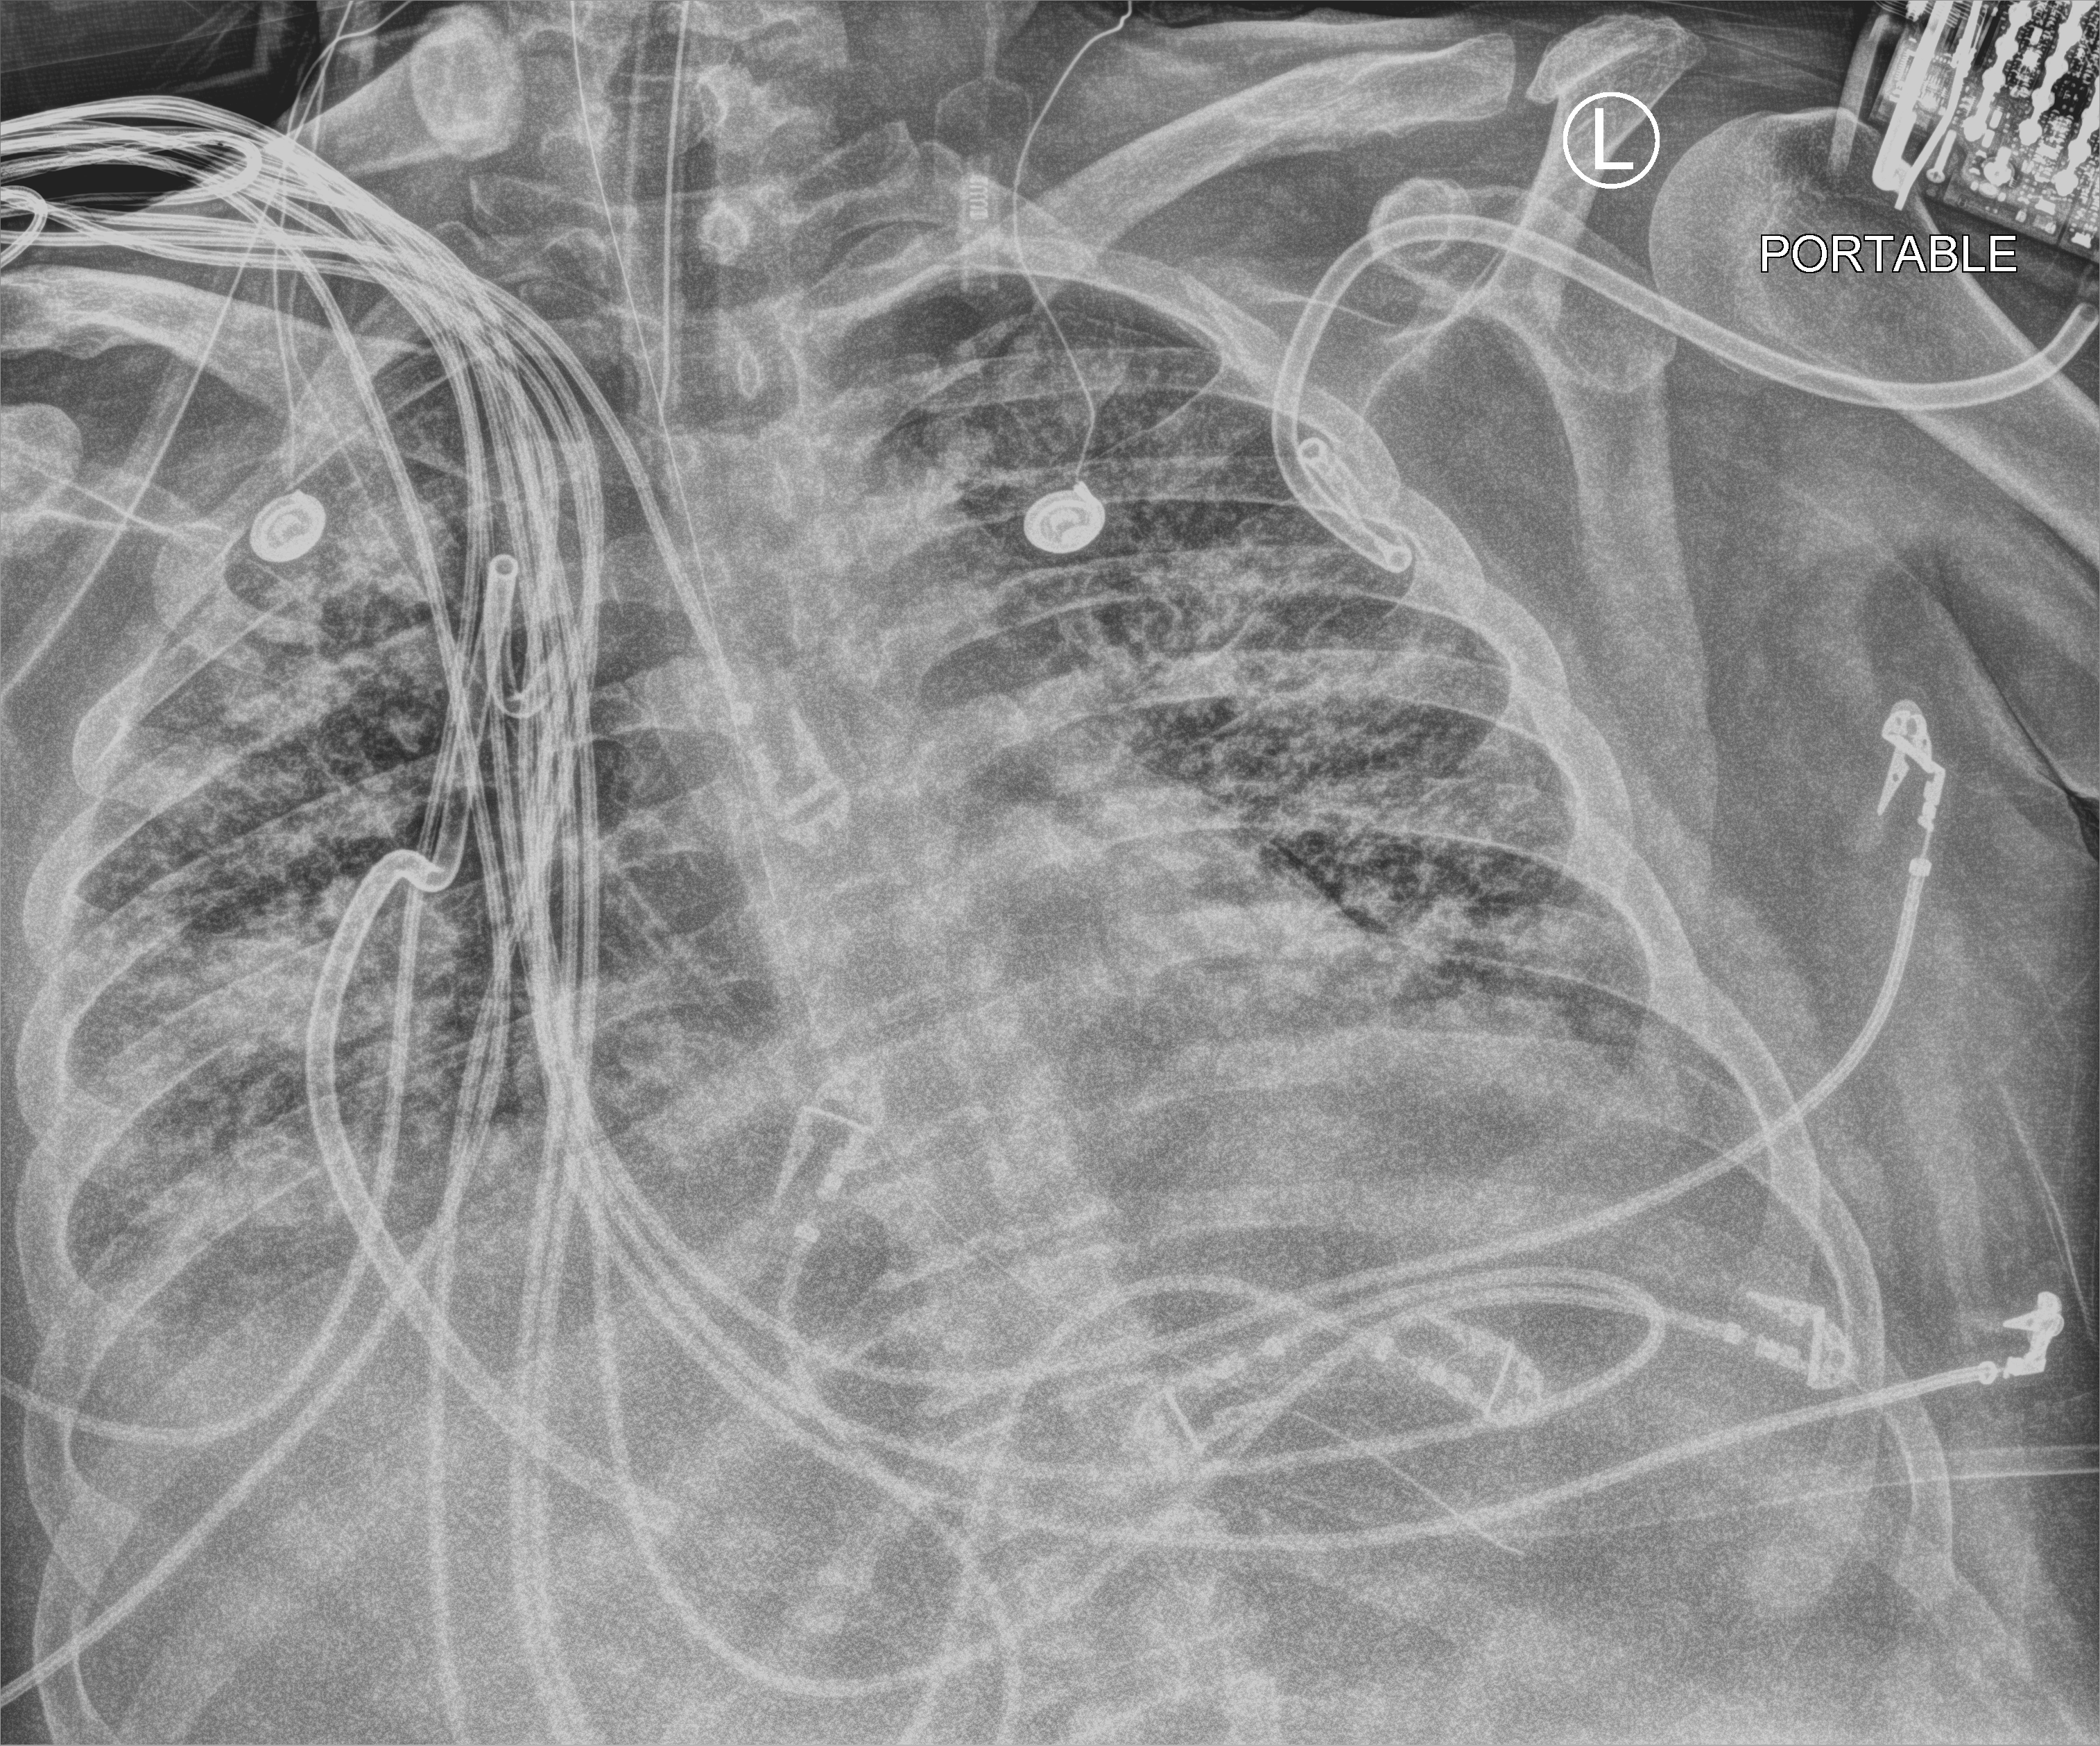
Bedside chest radiograph (computed radiography); anteroposterior (AP) projection. Patient hospitalised with COVID-19, aged 18–59 years.
From the hospital-stay record, not from the radiograph (when in the stay this image was taken is not recorded): mechanically ventilated during this hospital stay: yes; admitted to intensive care during this hospital stay: yes.